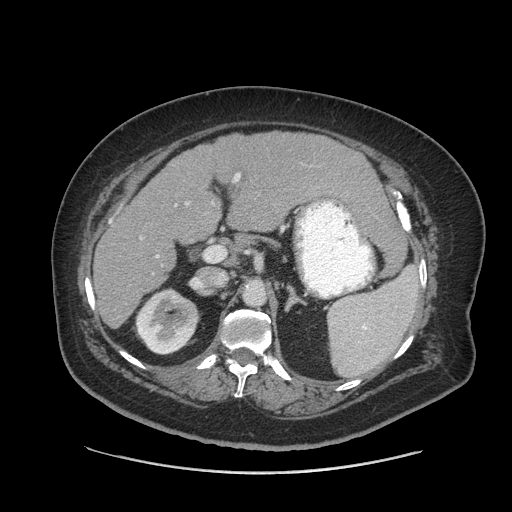
Contrast-enhanced abdominal CT (liver protocol), one axial slice; position 45 of 91 along the scan axis; reconstruction kernel STANDARD; 140 kVp; soft-tissue window (W 400 / L 40 HU); 2.5 mm slice thickness; 512 × 512 image matrix, field of view 420 × 420 mm. Case-level facts recorded for this patient, not image findings: diagnosis: hepatocellular carcinoma (patient treated with transarterial chemoembolisation; whether this scan precedes or follows treatment is not stated here); TNM stage (as recorded): Stage-I; Child-Pugh class: A; tumour differentiation: well differentiated.
Outlined on this slice (semi-automatically segmented with operator editing):
- liver parenchyma outside the tumour (the mass and vessels are separate outlines, so this box may not span the whole liver): bounding box (x1, y1, x2, y2) in pixels: (94, 132, 384, 328)
- liver vessels: (109, 173, 240, 258)